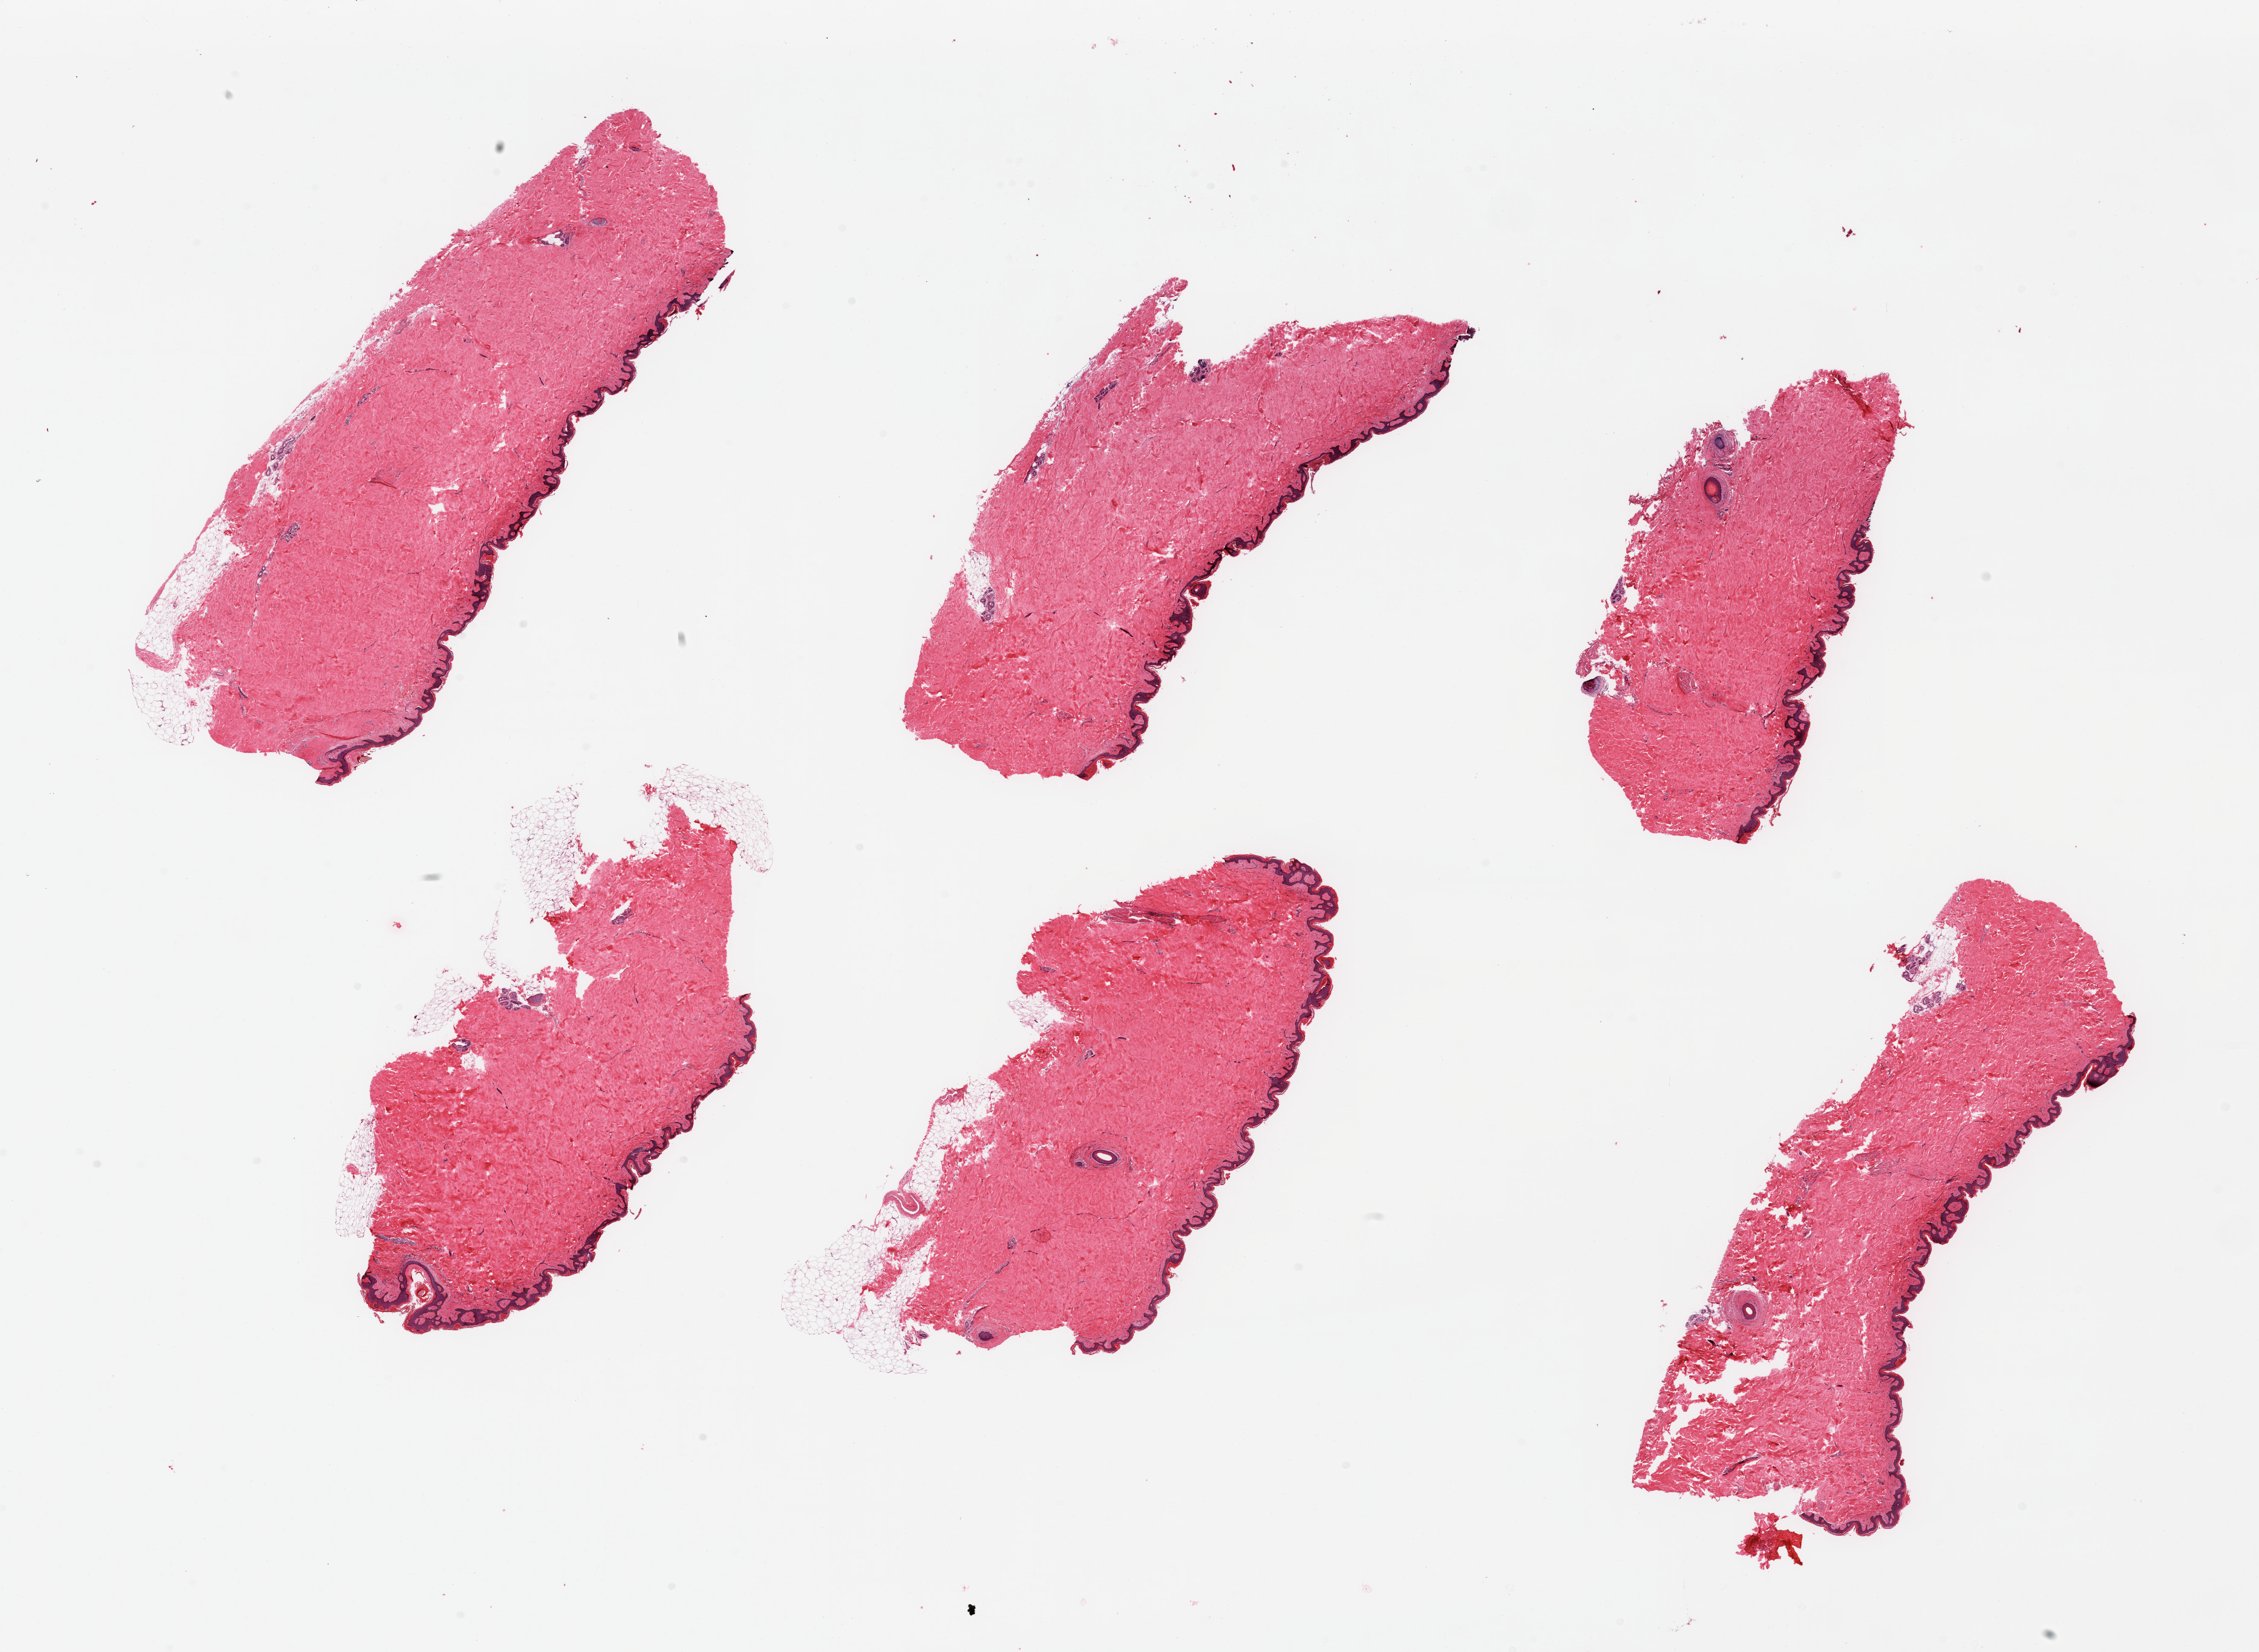
Whole-slide image, hematoxylin and eosin (H&E) stain, a low-resolution overview of the entire scanned area, about 29.5 x 21.6 mm, PAXgene-fixed, paraffin-embedded tissue, sampled site (target tissue): skin of suprapubic region, tissue donor sample.
Review note (as recorded): 6 pieces; few pieces include ~10% attached fat.